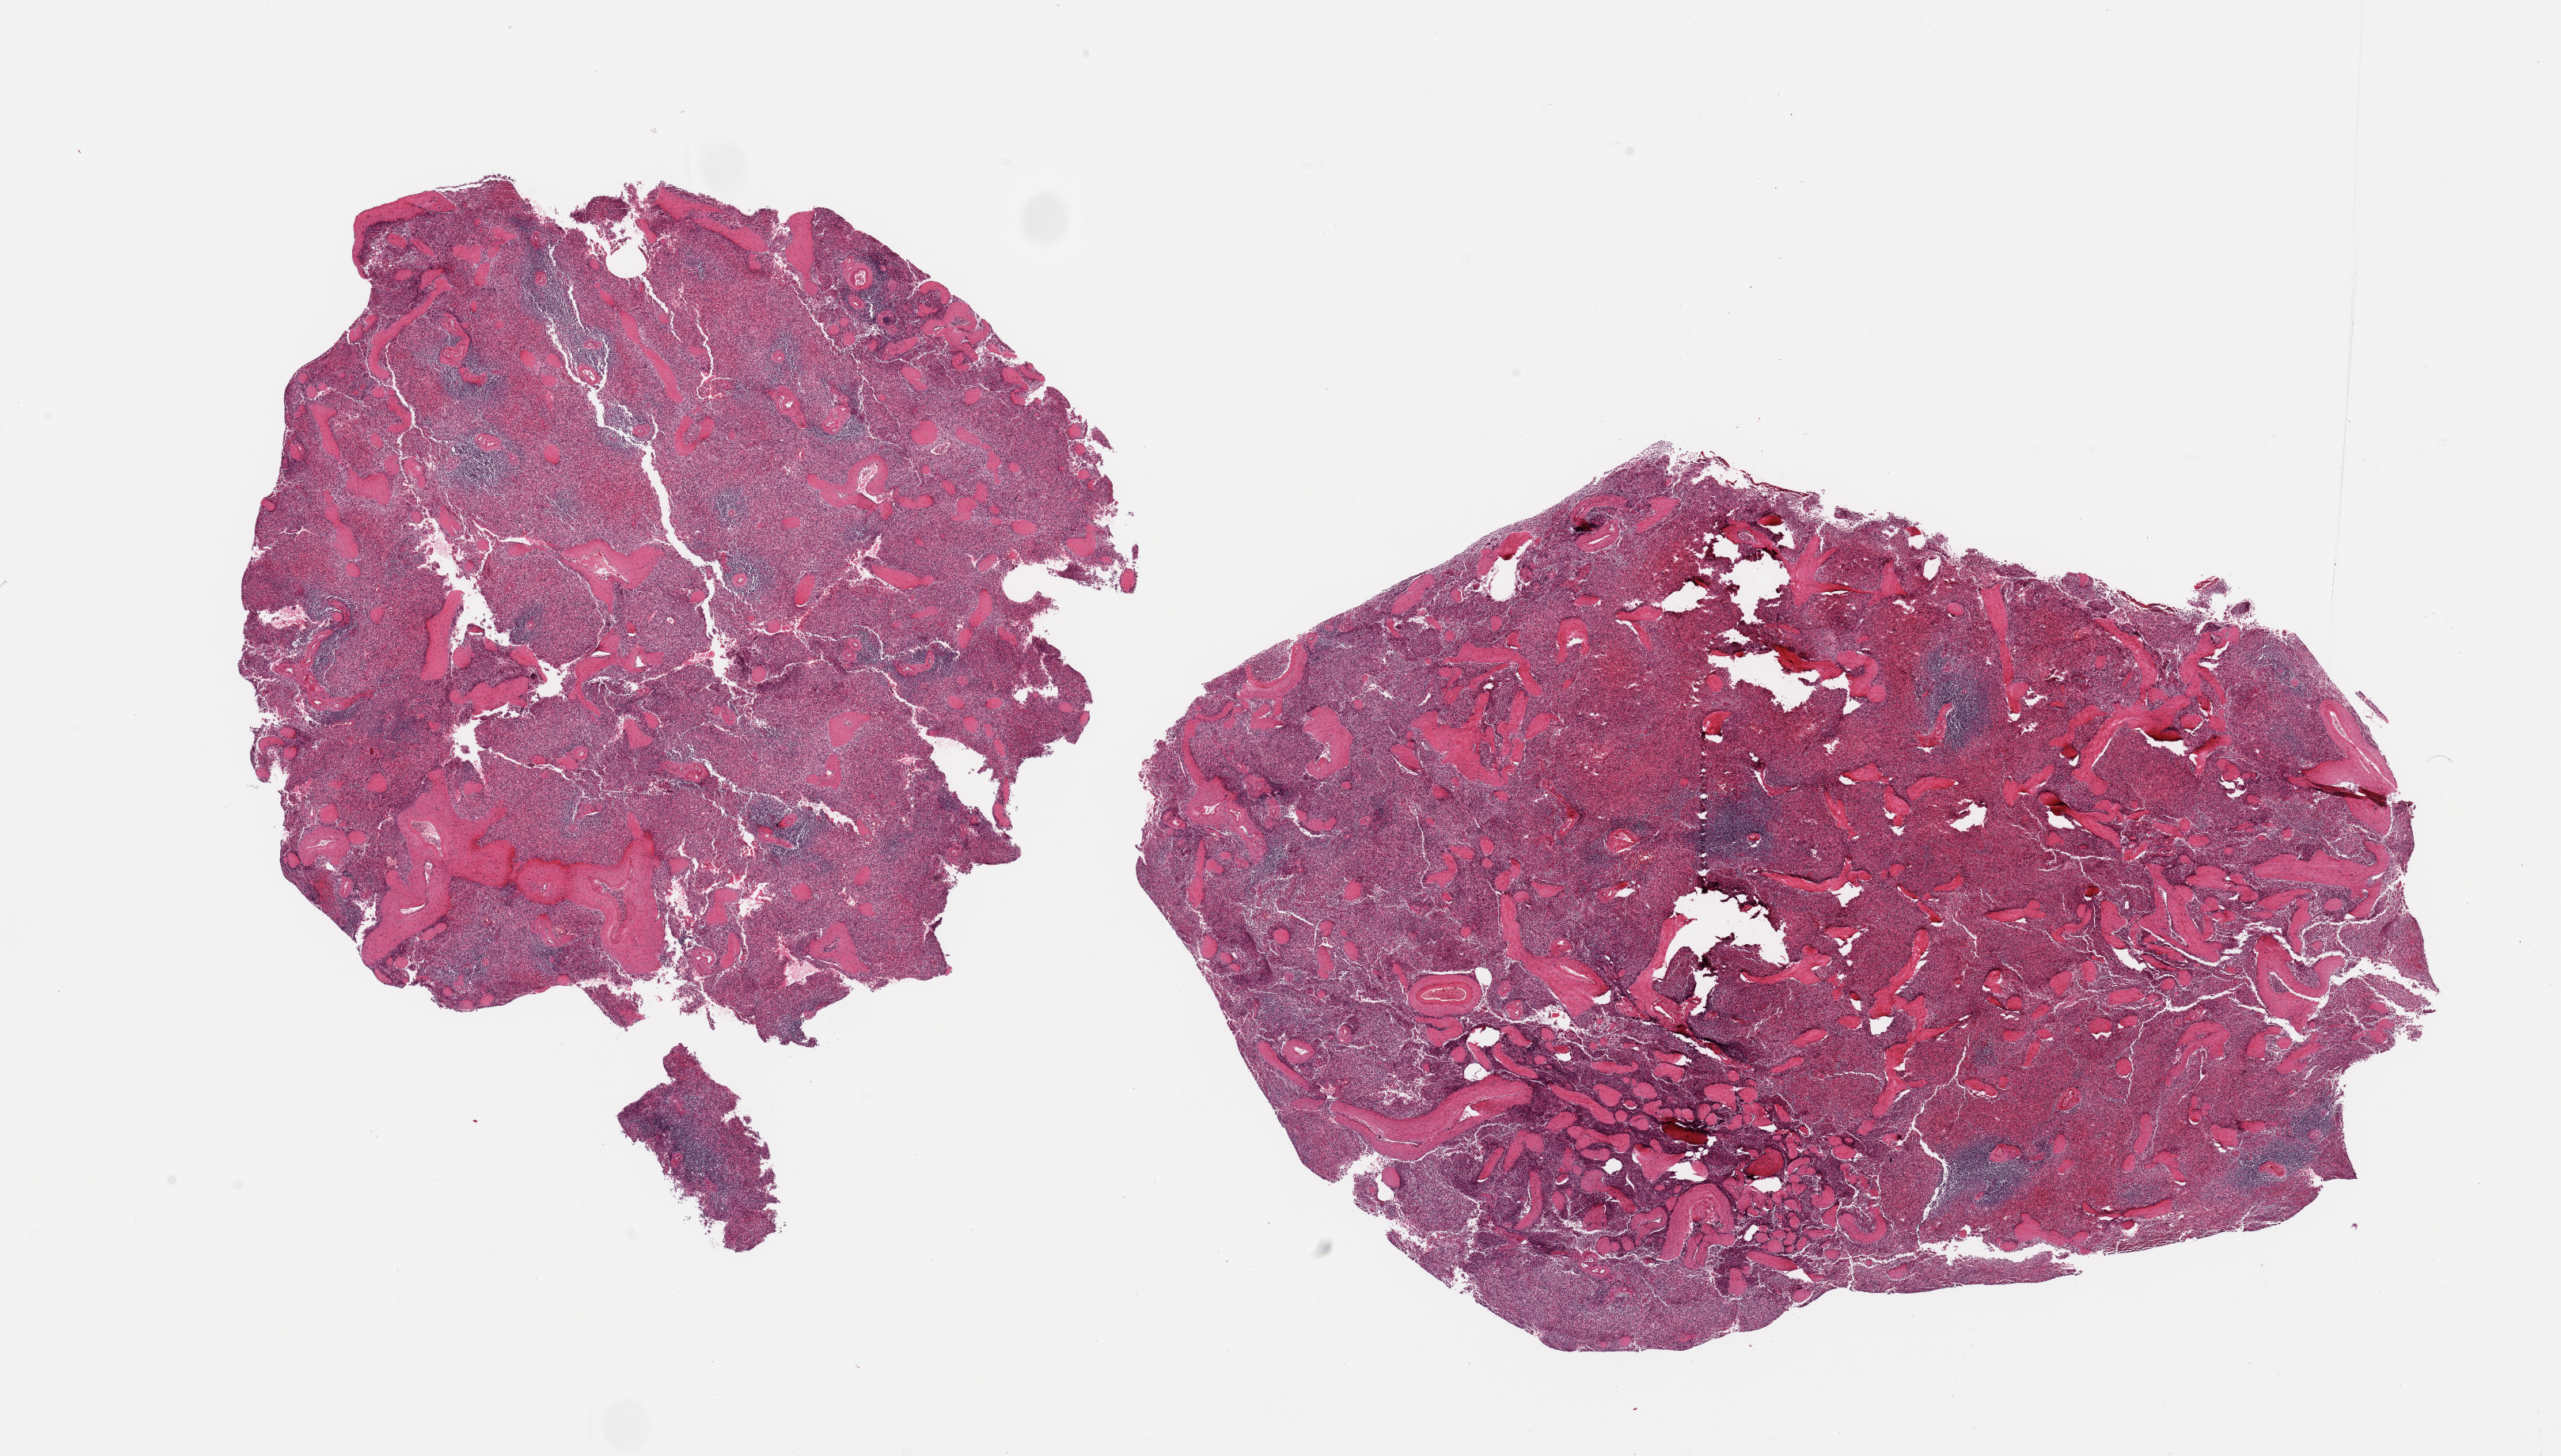
Hematoxylin and eosin (H&E) whole-slide image, low-resolution overview of the scanned area, about 25.6 x 14.6 mm (from a 20x scan). PAXgene-fixed, paraffin-embedded tissue. Section of spleen (target tissue). Tissue donor sample. Donor: male.
• review note (as recorded): 2 pieces, moderate congestion, hyalinizing fibrosis suggestive of old splenitis